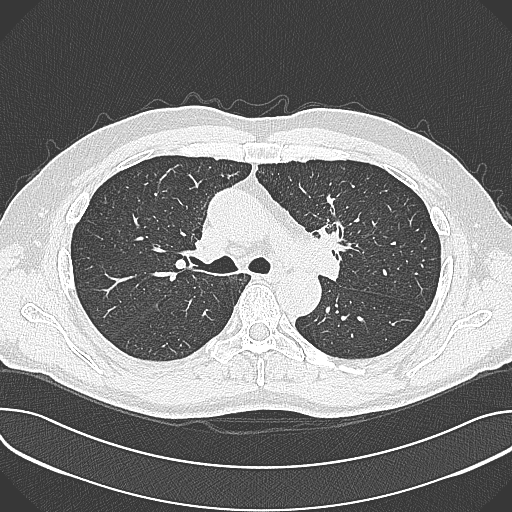
Chest CT (low-dose screening protocol), one axial image; baseline screening round; lung window (W 1500 / L -600 HU); 1 mm slice thickness; lung (sharp) reconstruction kernel (B80f); slice 118 of 361 in the series; 512 × 512 image matrix, field of view 380 × 380 mm. Male participant, aged 59 years at enrolment.
• Expert reader's lesion annotation, bounding box [x1, y1, x2, y2] px = [303, 192, 365, 256].
• The screening reader recorded 2 non-calcified nodules or masses ≥4 mm on this exam (left upper lobe, left upper lobe); which of them this box marks is not recorded.